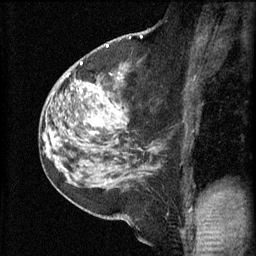
Breast MRI (dynamic contrast-enhanced), one sagittal slice. Slice 33 of 60 in the series (ordered by position). 3 images stored at this slice position (order not interpretable as contrast timing). 1.5 T. TE 4.2 ms, TR 11 ms. 256 × 256 image matrix, field of view 180 × 180 mm. Patient: female, 52 years.
Outlined on this slice (semi-automatically segmented with operator editing):
- analysis volume of interest (the breast-tissue region the enhancement analysis was run in; not a lesion): bounding box [x1, y1, x2, y2] px = [86, 76, 158, 157]
- tumour enhancement mask (voxels above the 70 % enhancement threshold inside the analysis volume of interest): [93, 118, 95, 121]